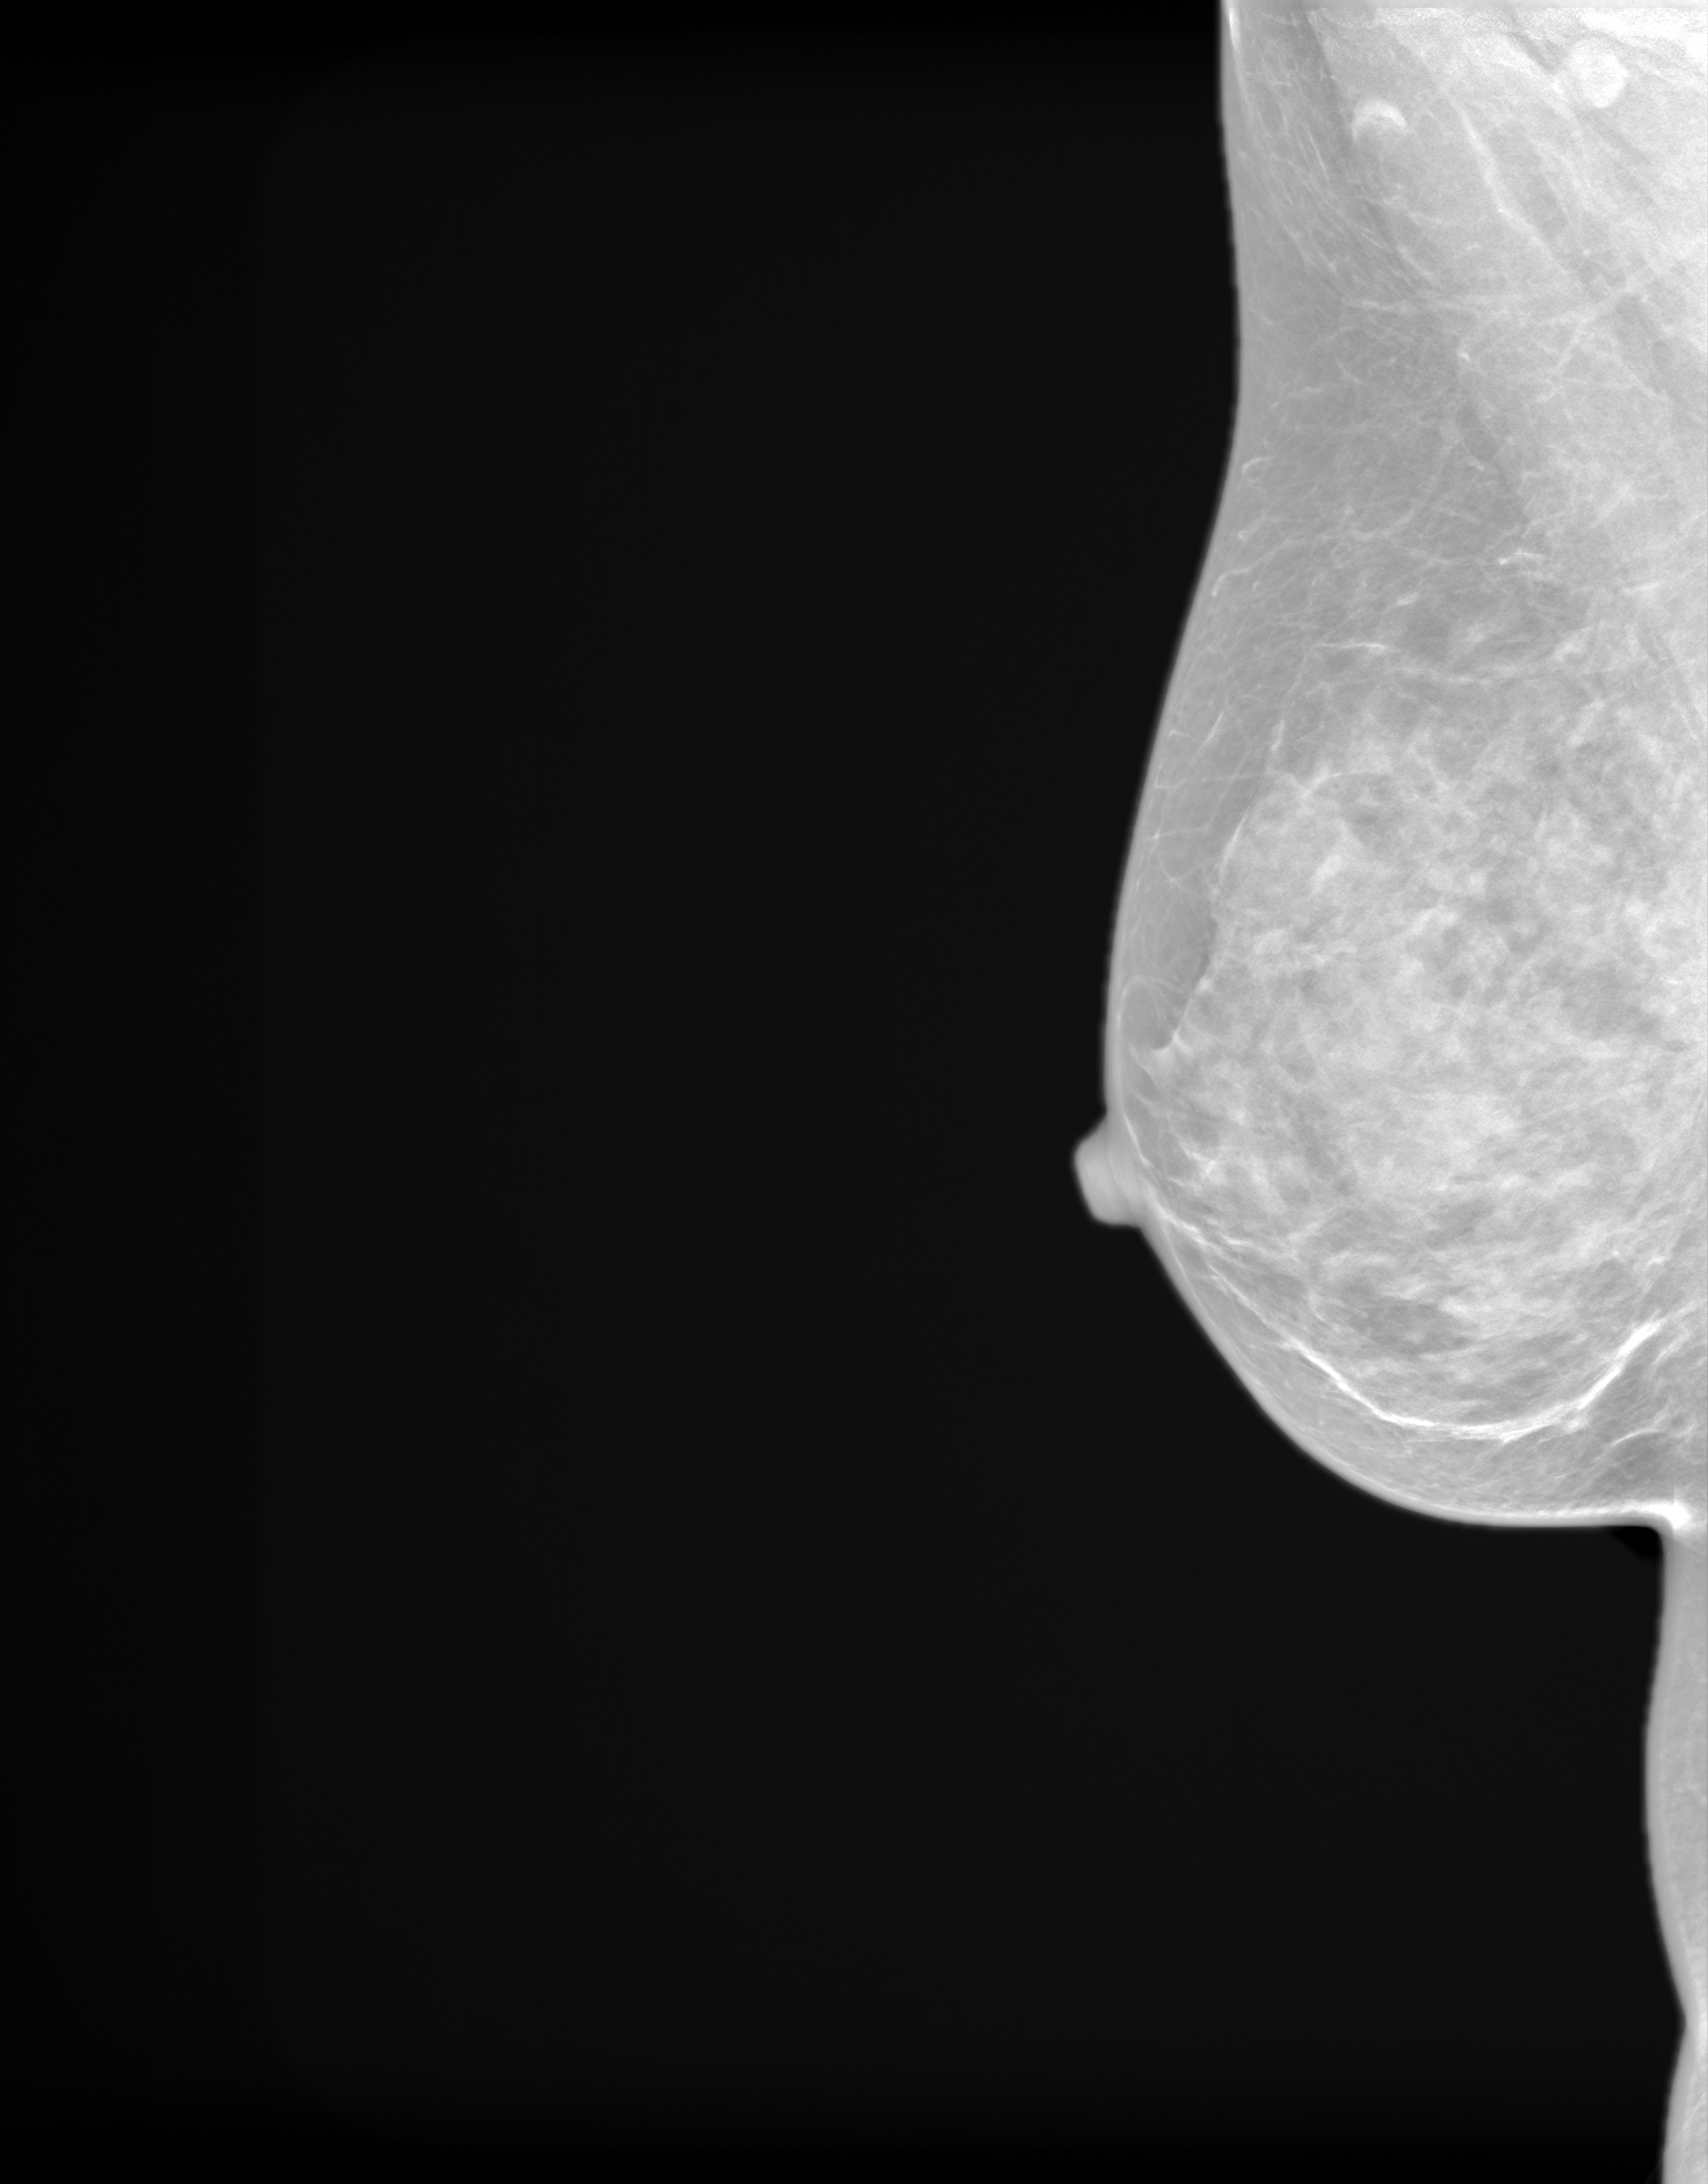
Screening examination, system: SenoIris_1SP2(440). Patient: female, 61 years.
Image type: synthesized 2-D view from tomosynthesis. Breast: right. Projection: mediolateral oblique (MLO) view.